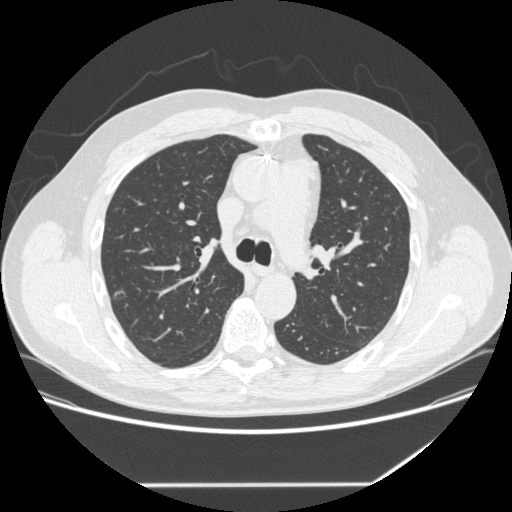
Chest CT (low-dose screening protocol), one axial image. Baseline annual screen. Lung window (W 1500 / L -600 HU). 1.25 mm slice thickness. Standard (soft-tissue) reconstruction kernel (STANDARD). Slice 94 of 262 in the series. 512 × 512 image matrix. Male, age 62 years at enrolment. Current smoker at enrolment.
• Lesion marked by an expert reader, bounding box (x1, y1, x2, y2) in pixels: (98, 281, 134, 310).
• No non-calcified nodule or mass ≥4 mm was recorded by the screening reader at this exam.
• Participant outcome: lung cancer diagnosed 839 days after this screen (after the third annual screen) — adenocarcinoma, NOS, right upper lobe, moderately differentiated (G2), stage IA (AJCC 6th edition), 12 mm at pathology.